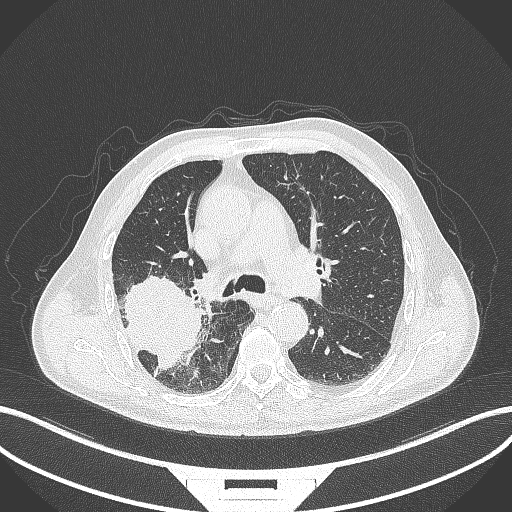
Chest CT, one axial slice; position 259 of 429 along the scan axis; reconstruction kernel B70f; lung window (W 1500 / L -600 HU); 1 mm slice thickness; 512 × 512 image matrix. Patient: male, 72 years. From the clinical record (not read from this slice): clinical TNM (as recorded): T3 N2 M0.
Structures marked on this image (rectangle marked by the reading radiologist):
- lung tumour (recorded histology: adenocarcinoma): box from (x=117, y=275) to (x=208, y=374) px